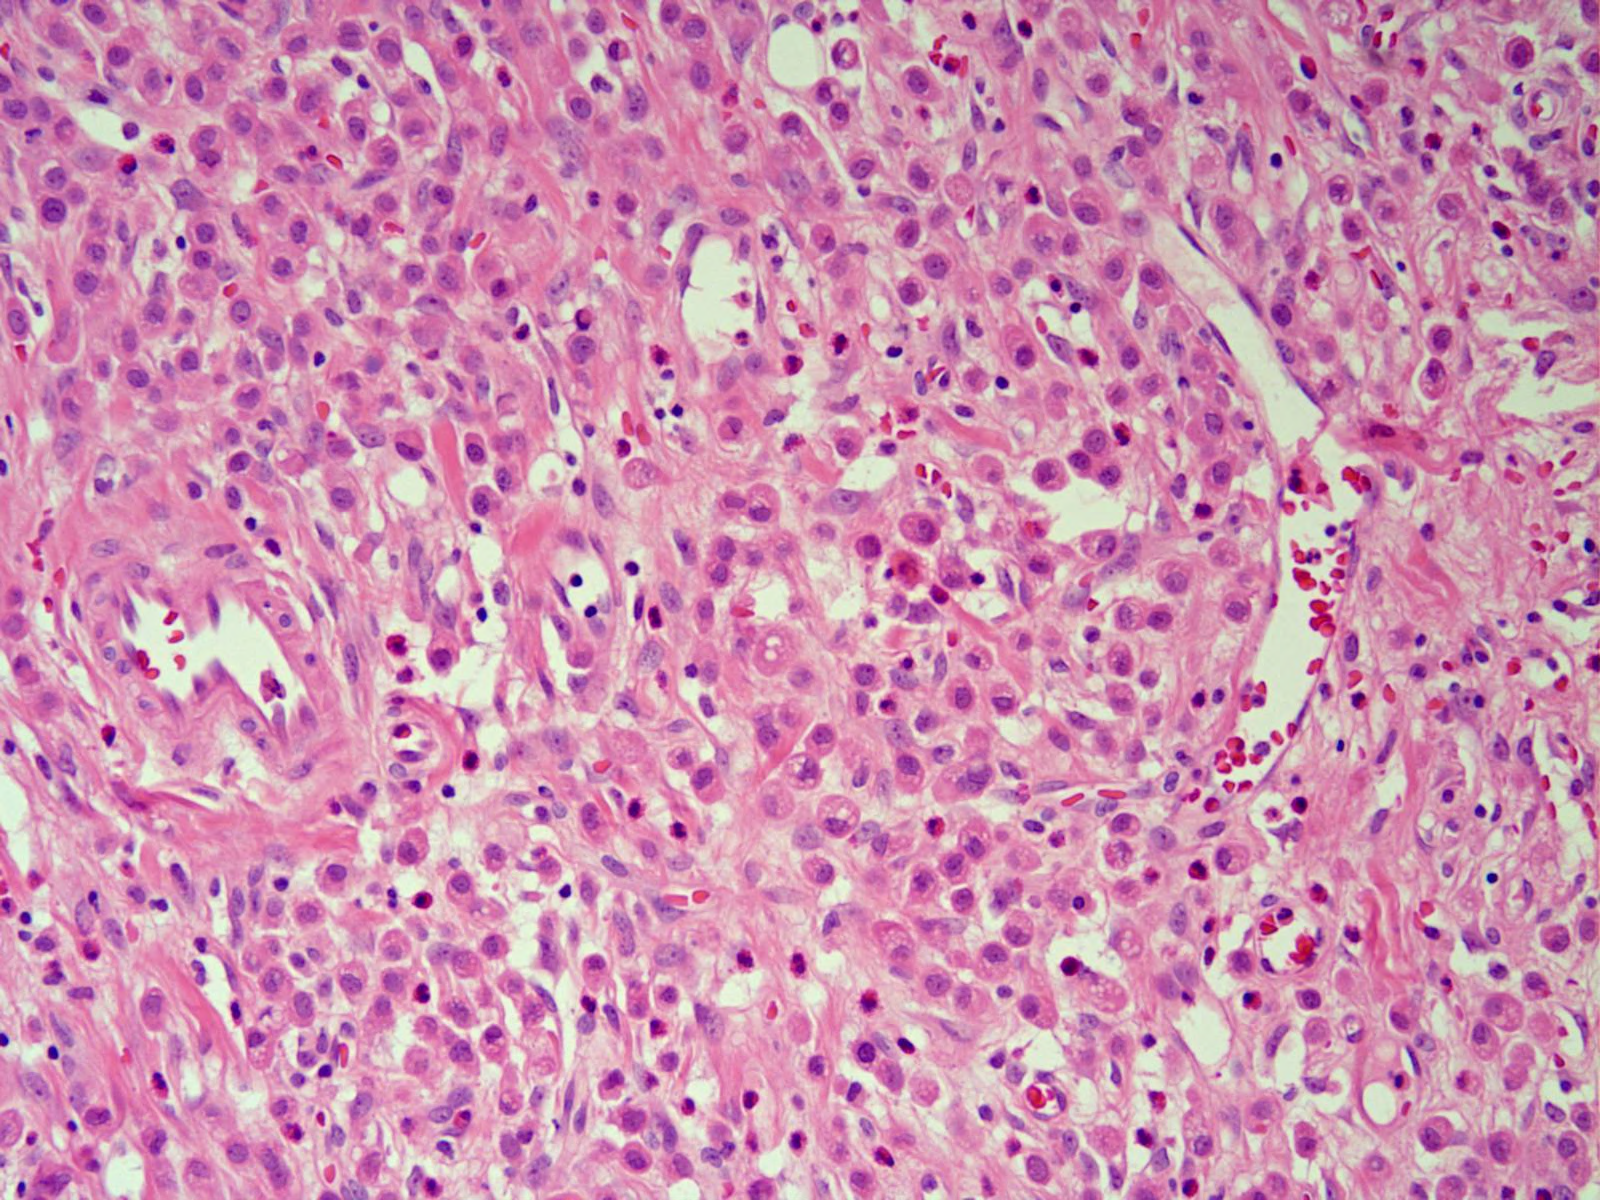
Single-field H&E photomicrograph — about 0.8 x 0.6 mm across. Formalin-fixed paraffin-embedded (FFPE) diagnostic section. Primary tumour sample from the stomach. Male patient; age at initial diagnosis 56 years. Histologic grade: G3 (poorly differentiated).
* histologic diagnosis: Adenocarcinoma, NOS